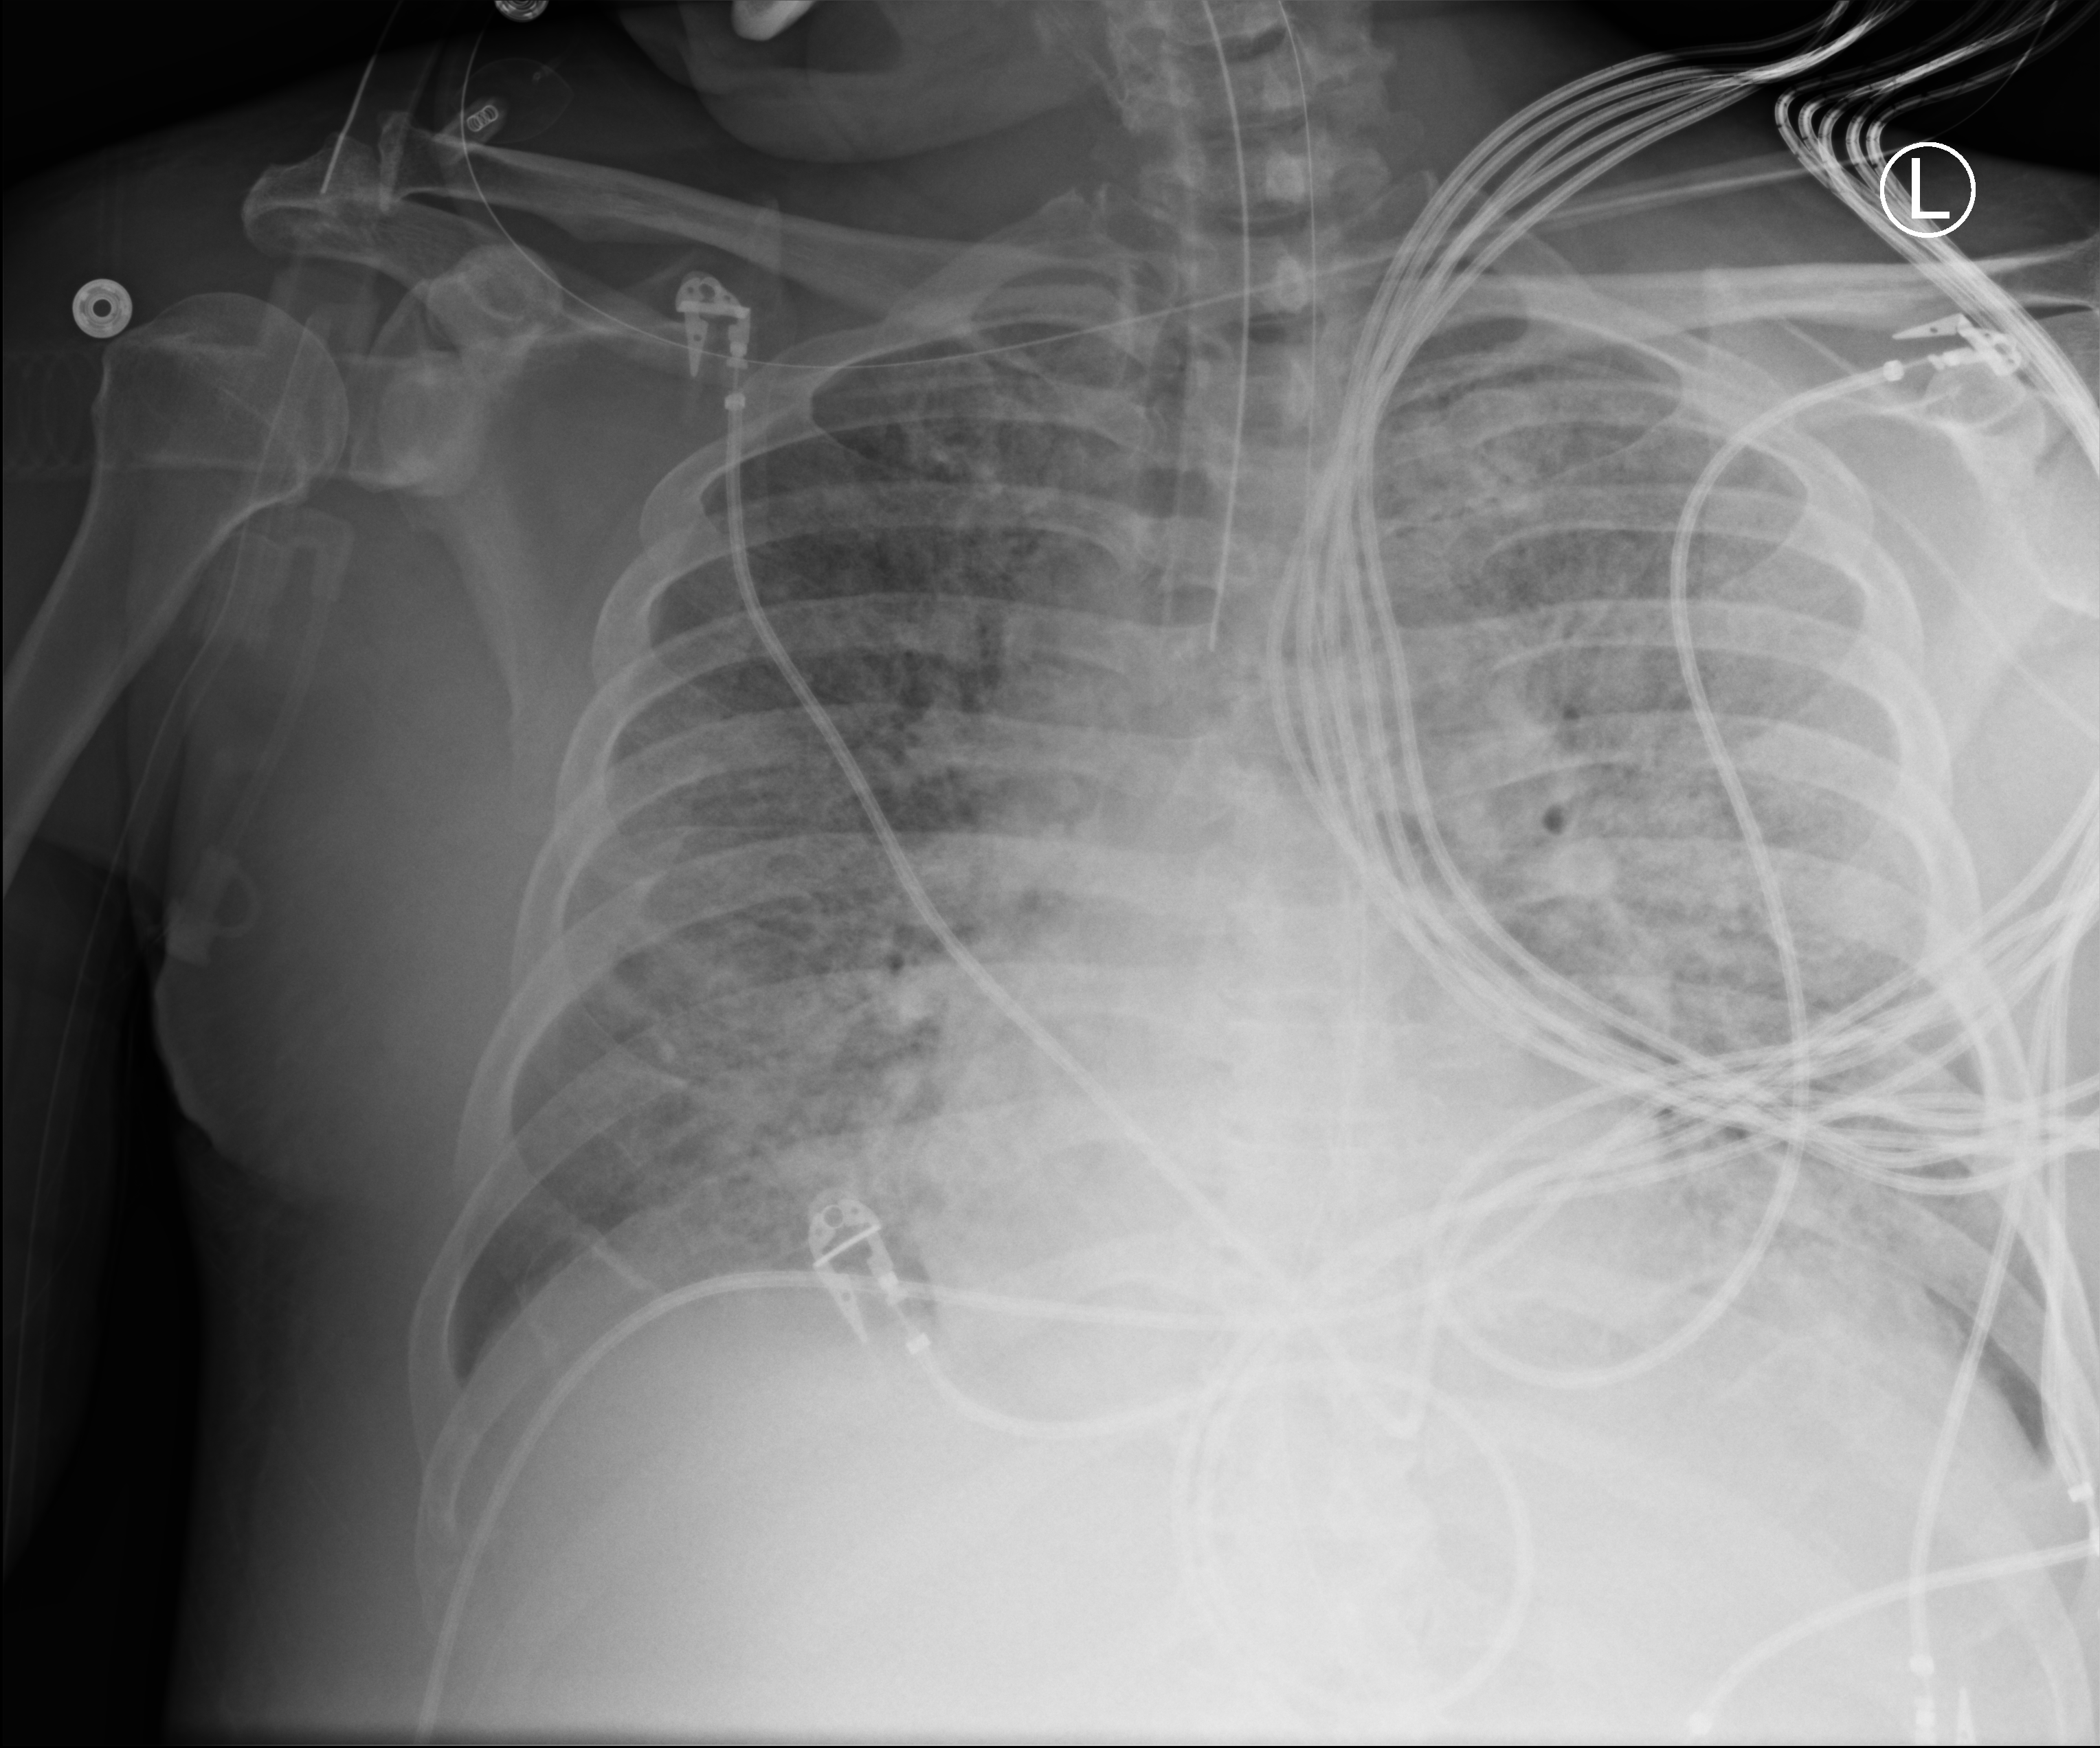
Portable chest radiograph, anteroposterior (AP) projection. Male patient hospitalised with COVID-19, age 60–74 years.
From the hospital-stay record, not from the radiograph (when in the stay this image was taken is not recorded): mechanically ventilated during this hospital stay: yes; admitted to intensive care during this hospital stay: yes; other chronic lung disease (admission record): no.